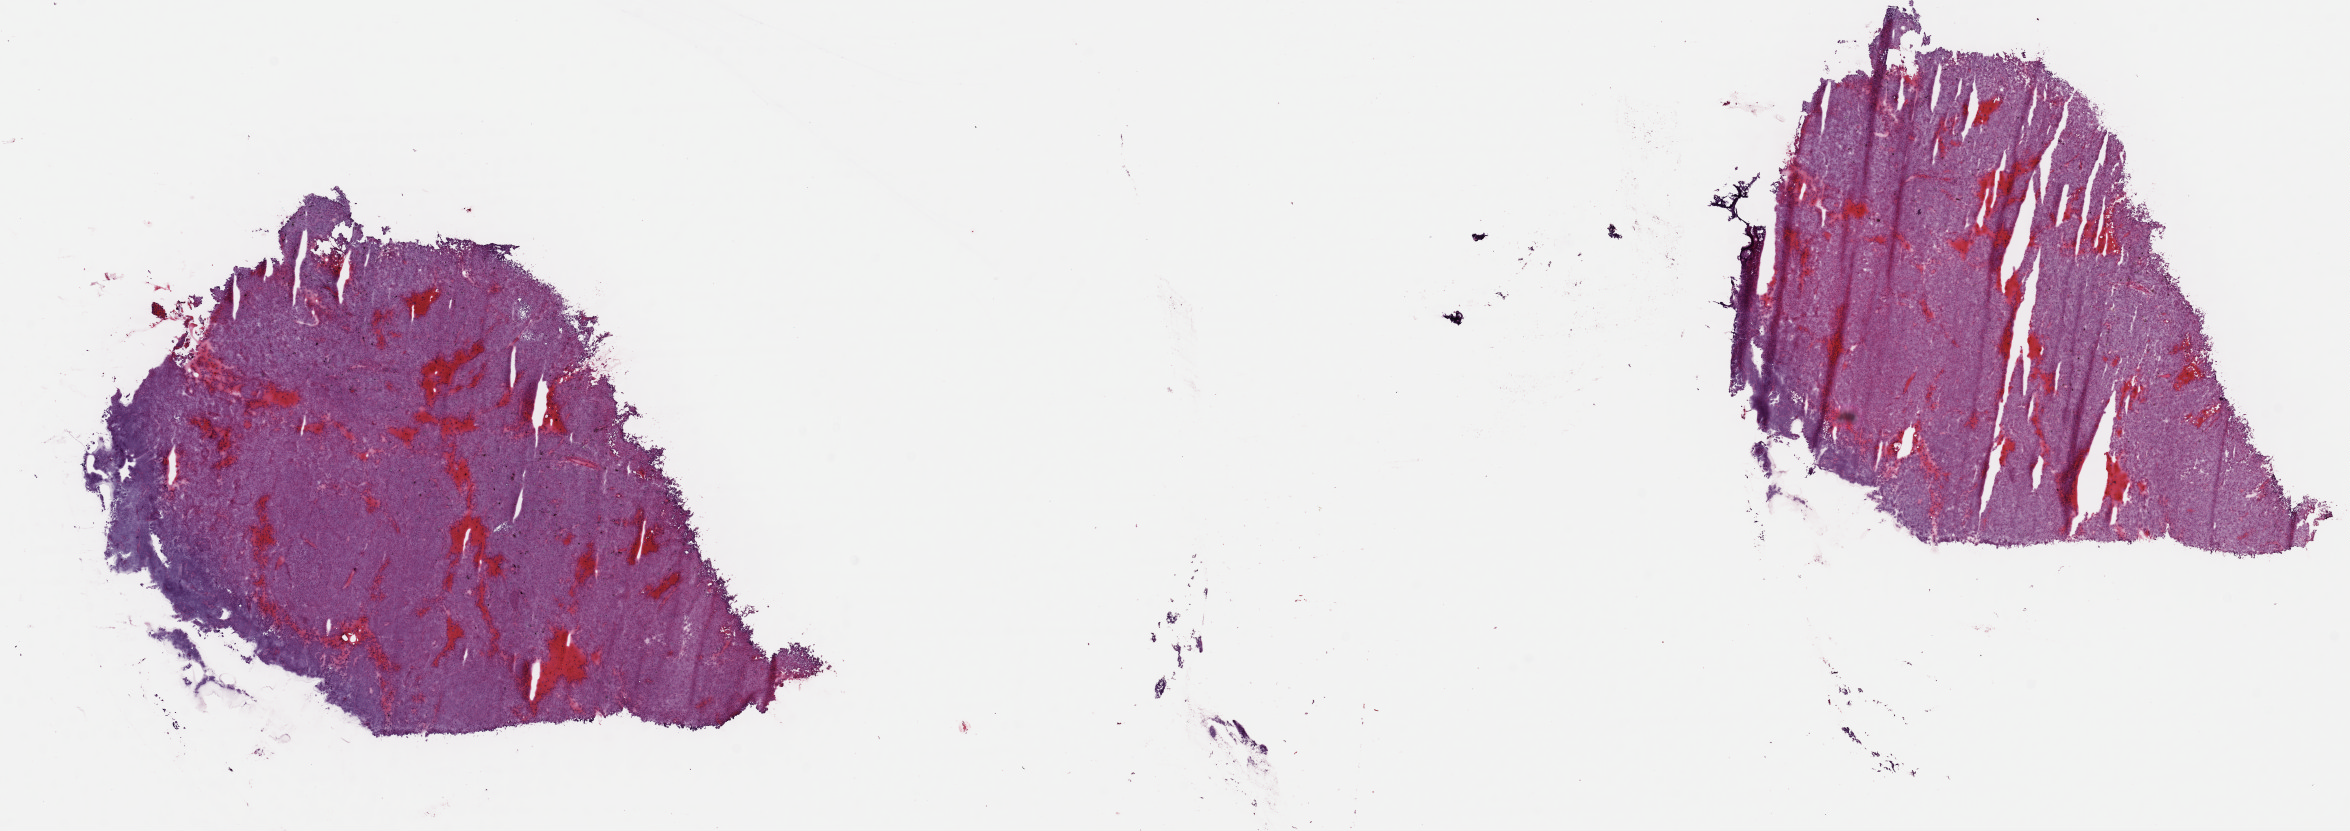
Whole-slide histology image, H&E — a low-resolution overview of the entire scanned area, about 18.6 x 6.6 mm (slide scanned at 40x); frozen section from the top of the tissue portion; metastatic tumour sample, sampled site: lymph node. Female patient; age at initial diagnosis 60 years. Pathologist review of this section (percent, as recorded): tumour cells 100%, tumour nuclei 97%, normal cells 0%, stromal cells 0%, necrosis 0%. Infiltration values recorded for this section: lymphocyte infiltration 0%, monocyte infiltration 0%, neutrophil infiltration 0%.
This section: metastatic tumour tissue. Patient diagnosis: Malignant melanoma, NOS.